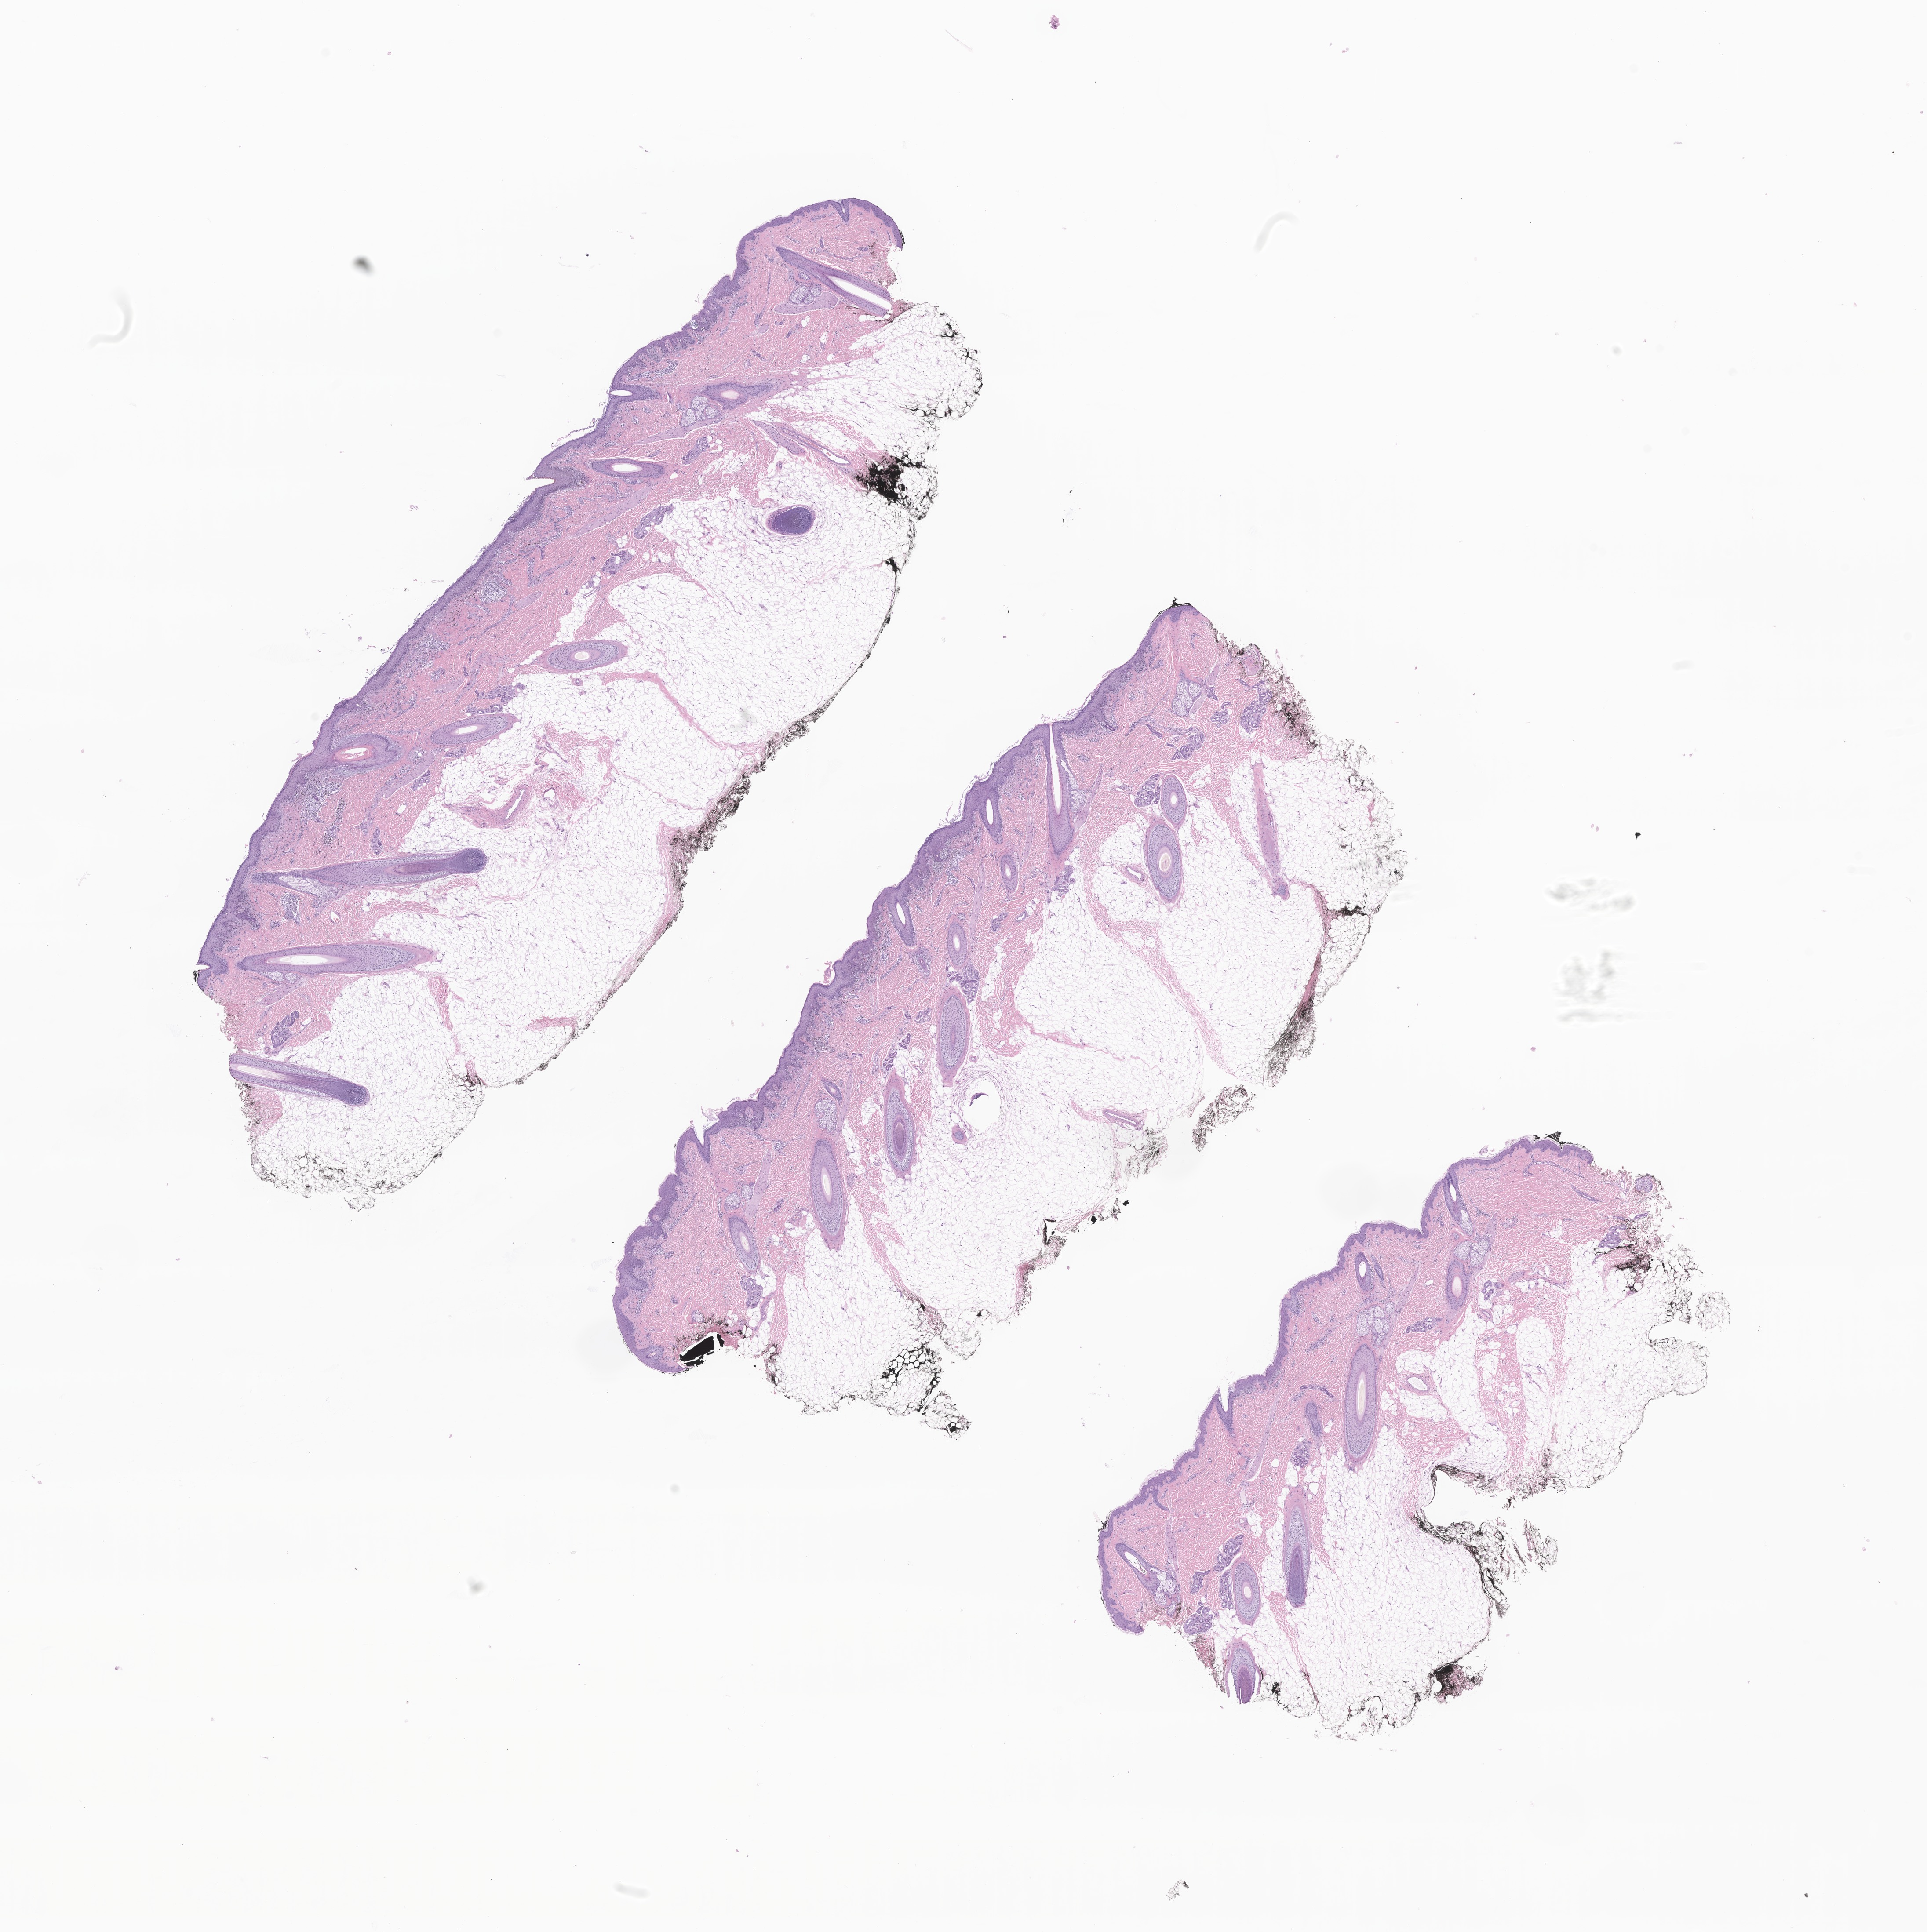
Digitized haematoxylin and eosin-stained section of tumor tissue from the skin of scalp and neck, low-resolution overview of the scanned area, about 18.5 x 18.5 mm; formalin-fixed, paraffin-embedded (FFPE) tissue. Female patient, age 120 months (10 years).
* diagnosis (ICD-O-3 morphology term): Low cumulative sun damage melanoma